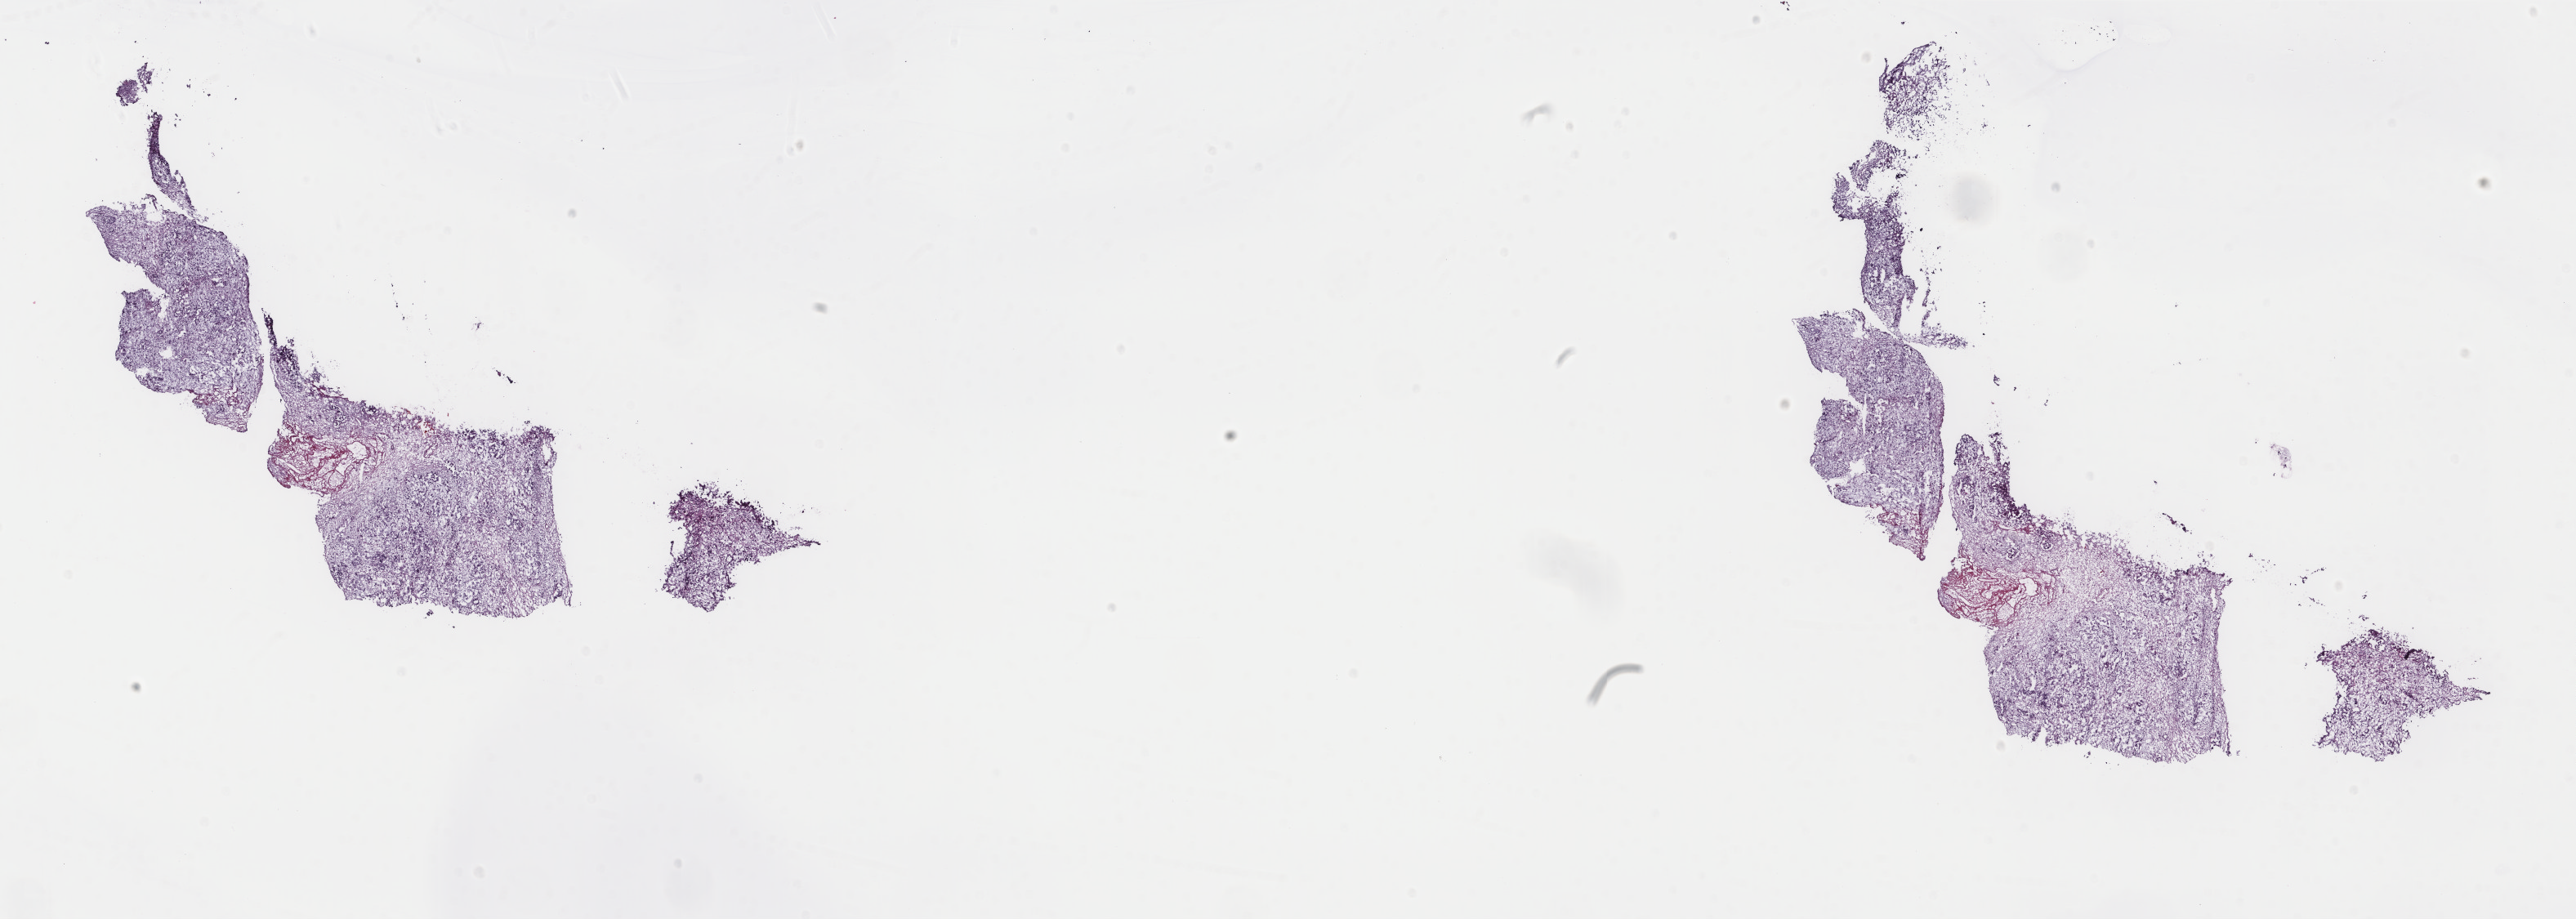
Whole-slide histology image, Hematoxylin and eosin (H&E) stained — a low-resolution overview of the entire scanned area, about 25.0 x 8.9 mm, frozen section, sample: primary tumour, uterus. Female, age 62 years at initial diagnosis. Composition of this section per pathologist review: tumour cells 90%, tumour nuclei 80%, normal cells 0%, stromal cells 0%, necrosis 10%. Inflammatory infiltration, as recorded: lymphocyte infiltration 2%, monocyte infiltration 0%, neutrophil infiltration 0%.
FIGO stage: III. Histologic diagnosis: Mesodermal mixed tumor.